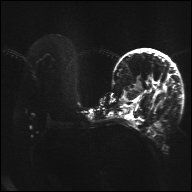
Breast MRI, one axial slice. Position 20 of 32 along the scan axis. Diffusion-weighted series; image 2 of 4 stored at this slice position (different b-values; order by instance number). 1.5 T. 192 × 192 image matrix, field of view 360 × 360 mm. Female patient.
Annotated regions visible in this slice (manually delineated by an expert):
- tumour on diffusion-weighted imaging: bounding box <151,77,153,81> (left, top, right, bottom; pixels)